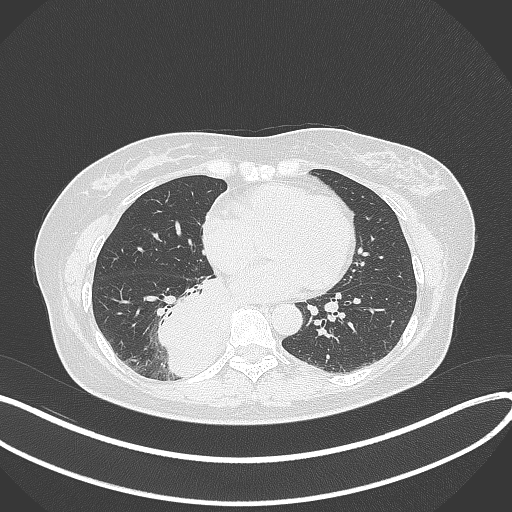
Chest CT, one axial slice. Position 143 of 331 along the scan axis. Lung window (W 1500 / L -600 HU). 1 mm slice thickness. 512 × 512 image matrix. Patient: female, 54 years. Case-level facts recorded for this patient, not image findings: clinical TNM (as recorded): T4 N0 M0.
Structures marked on this image (rectangle marked by the reading radiologist):
- lung tumour (recorded histology: adenocarcinoma): bounding box (x1, y1, x2, y2) in pixels: (157, 268, 234, 379)